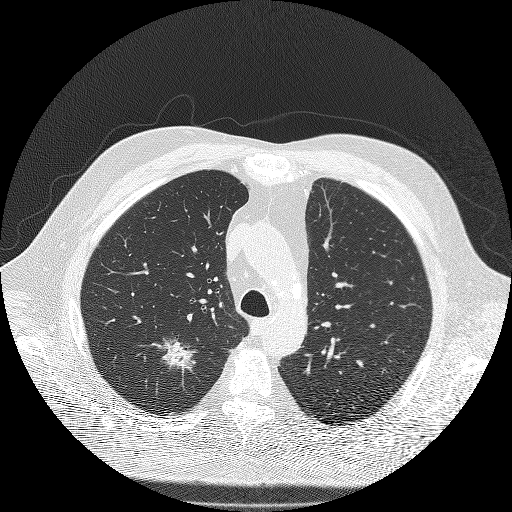
Axial slice from a low-dose chest CT screening exam; second annual screen; lung window (W 1500 / L -600 HU); 2 mm slice thickness; lung (sharp) reconstruction kernel (FC51); 120 kVp. Male participant, aged 71 years at enrolment. Former smoker at enrolment.
• Expert-annotated lung lesion, bounding box (x1, y1, x2, y2) in pixels: (137, 325, 207, 388).
• The screening reader recorded 3 non-calcified nodules or masses ≥4 mm on this exam (right upper lobe, right upper lobe, right lower lobe); which of them this box marks is not recorded.
• Official screen result: positive, other.
• Lung cancer was diagnosed 59 days after this screen: bronchiolo-alveolar adenocarcinoma, NOS, right upper lobe, moderately differentiated (G2), stage IIIA (AJCC 6th edition), 25 mm at pathology.